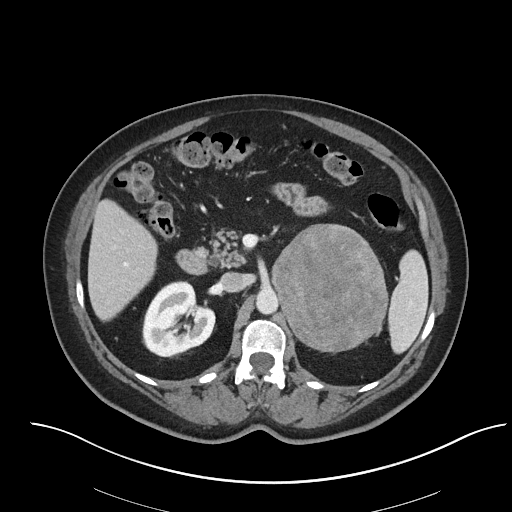
Contrast-enhanced abdominal CT, one axial slice. Position 43 of 92 along the scan axis. 120 kVp. Intravenous contrast given. Soft-tissue window (W 400 / L 40 HU). 3 mm slice thickness. 512 × 512 image matrix, field of view 440 × 440 mm. Female patient, age 53 years. Case-level facts recorded for this patient, not image findings: diagnosis: adrenocortical carcinoma; tumour side: left adrenal; tumour size at pathology: 9 cm; Ki-67 index: 28 %; stage (as recorded): 2.
Outlined on this slice (semi-automatically segmented with operator editing):
- mass: bounding box (x1, y1, x2, y2) in pixels: (272, 225, 387, 349)